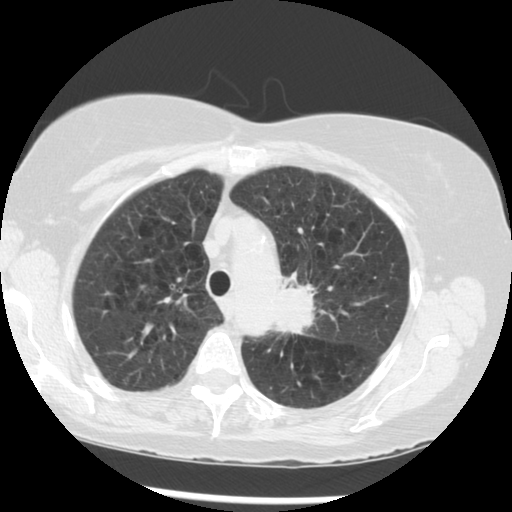
Low-dose screening chest CT, one axial slice. Slice 215 of 283 in the series (ordered by position). Lung window (W 1500 / L -600 HU). 512 × 512 image matrix.
Outlined on this slice (outlined manually by an expert reader):
- lesion 1 (tumor, upper lobe of left lung): bounding box <274,274,314,334> (left, top, right, bottom; pixels)